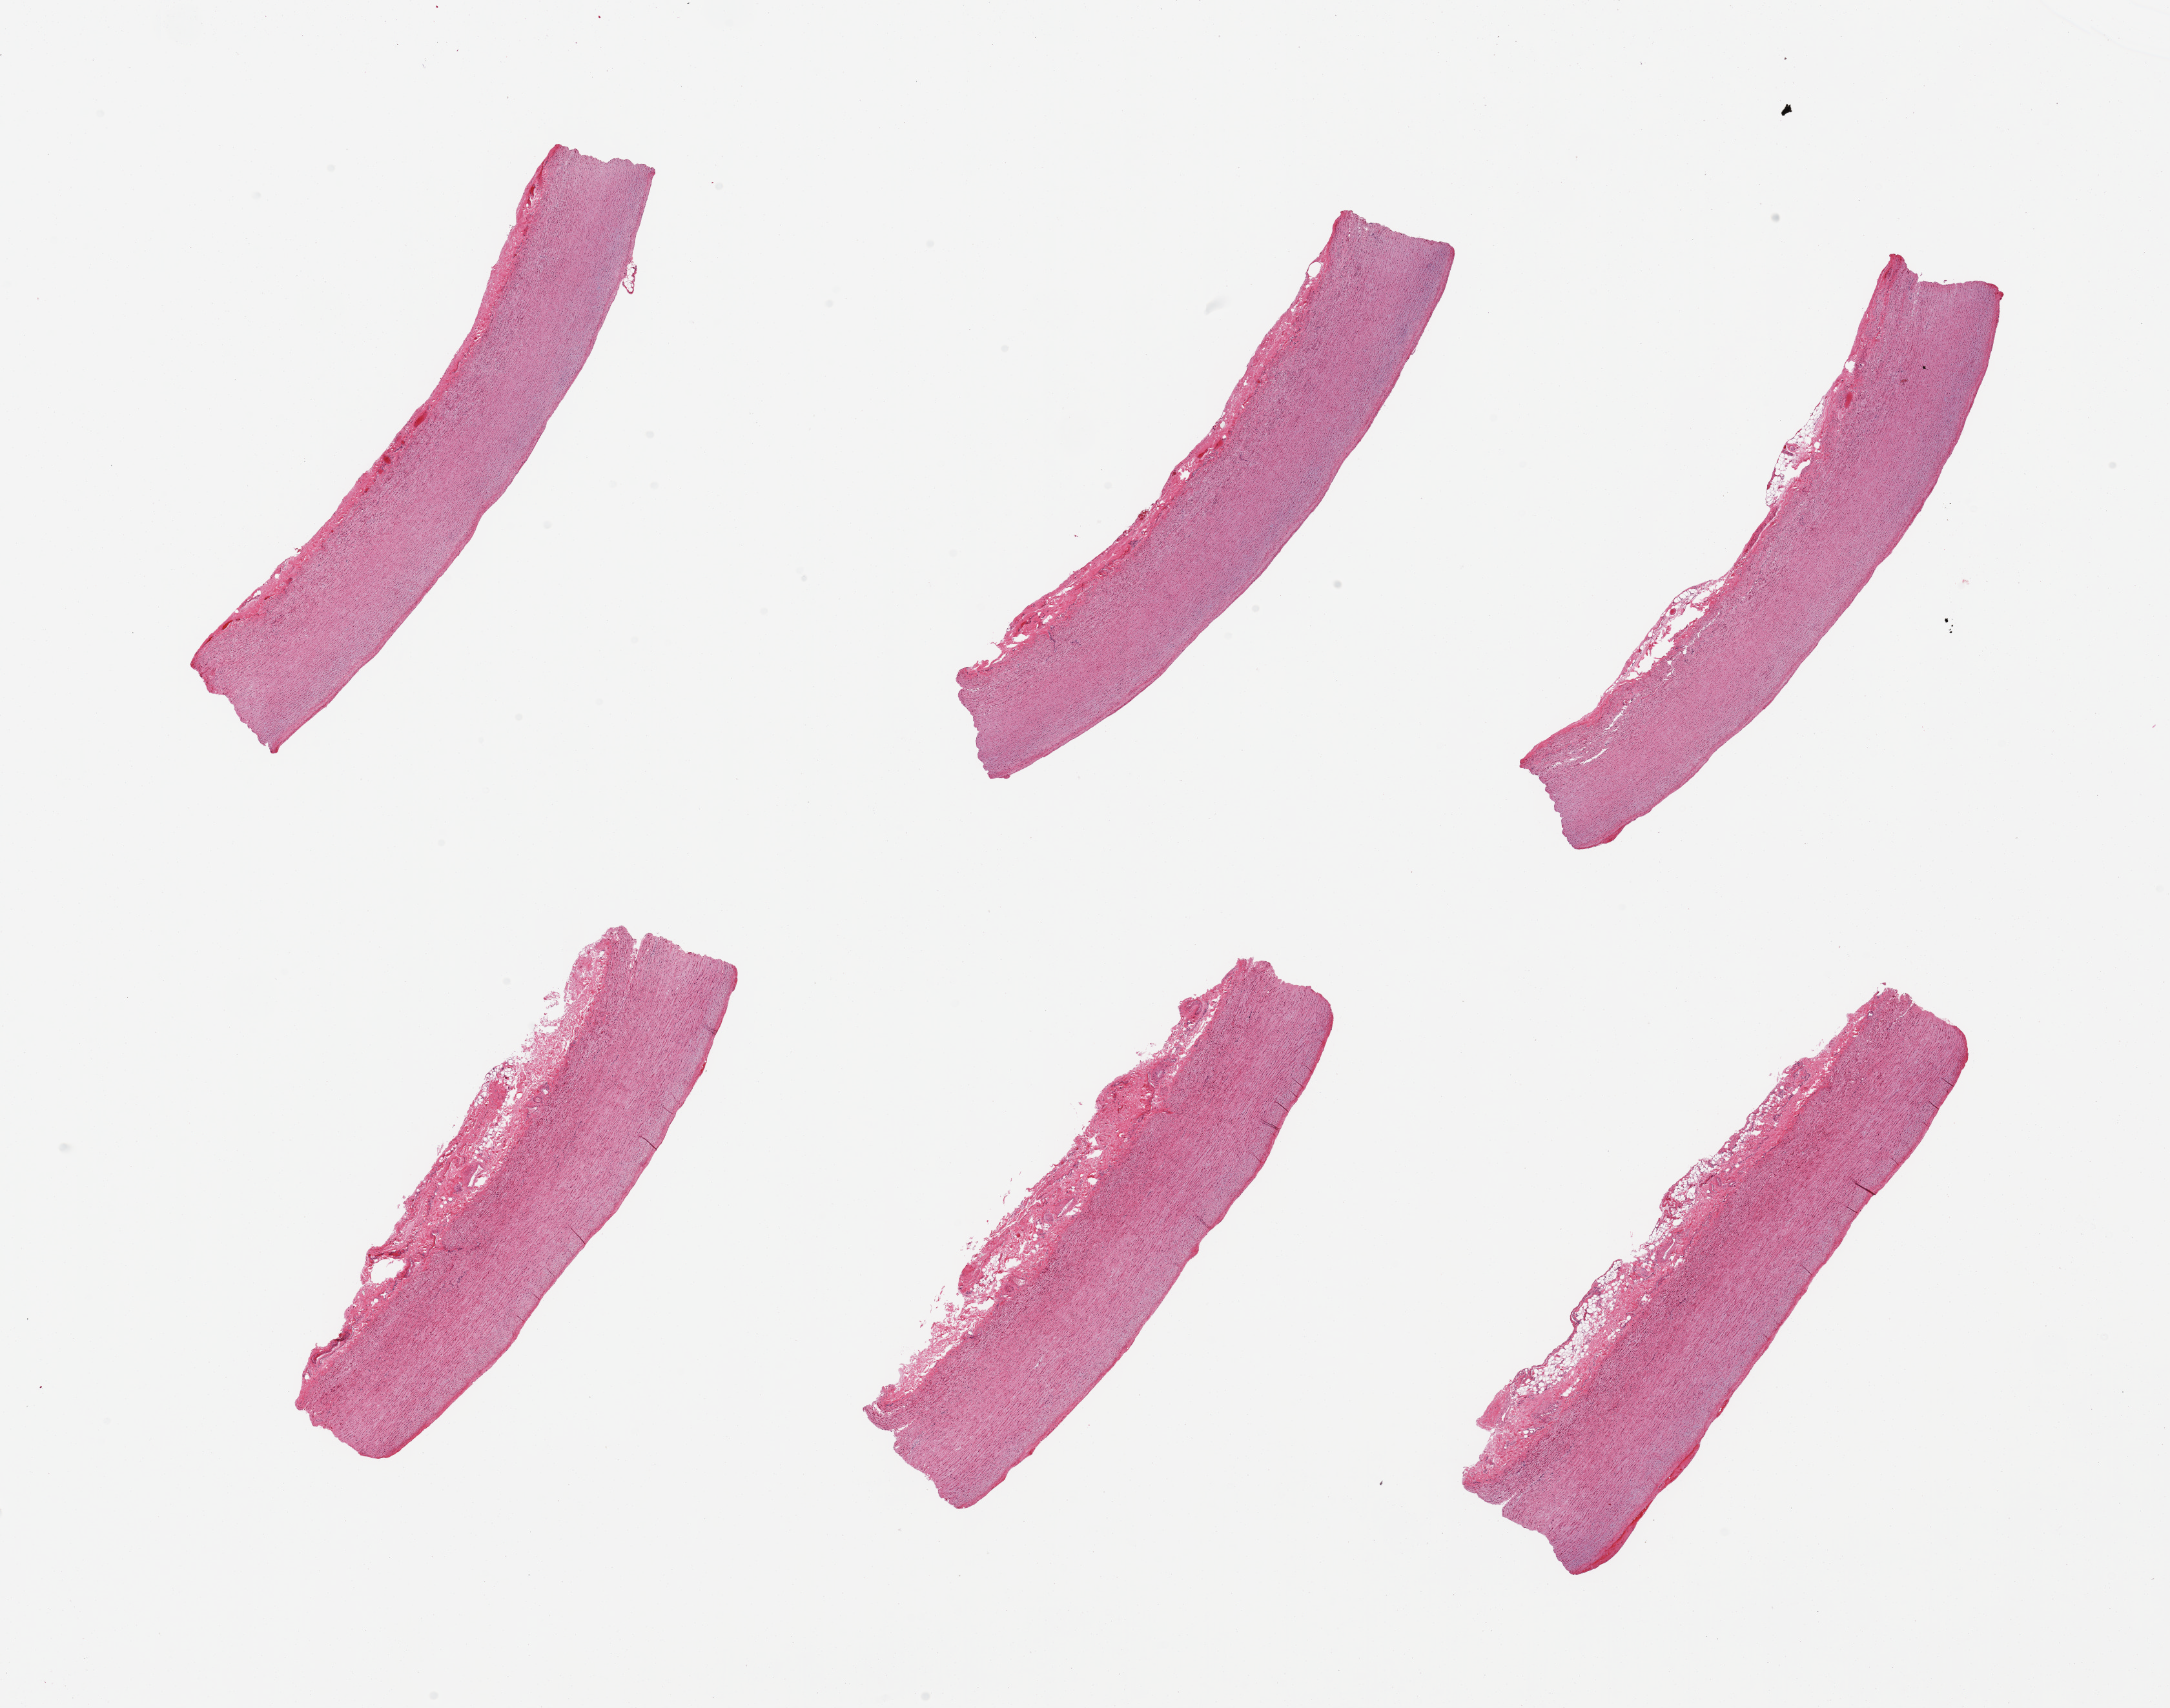
H&E whole-slide image, low-resolution overview of the scanned area, about 26.6 x 20.9 mm (slide scanned at 20x); PAXgene-fixed paraffin-embedded (PFPE) section; target tissue: aorta; donor tissue sample. Donor: male.
Reviewer comment on this tissue sample: 6 pieces: largely plaque-free; up to 0.6 fibrofatty adventitia.